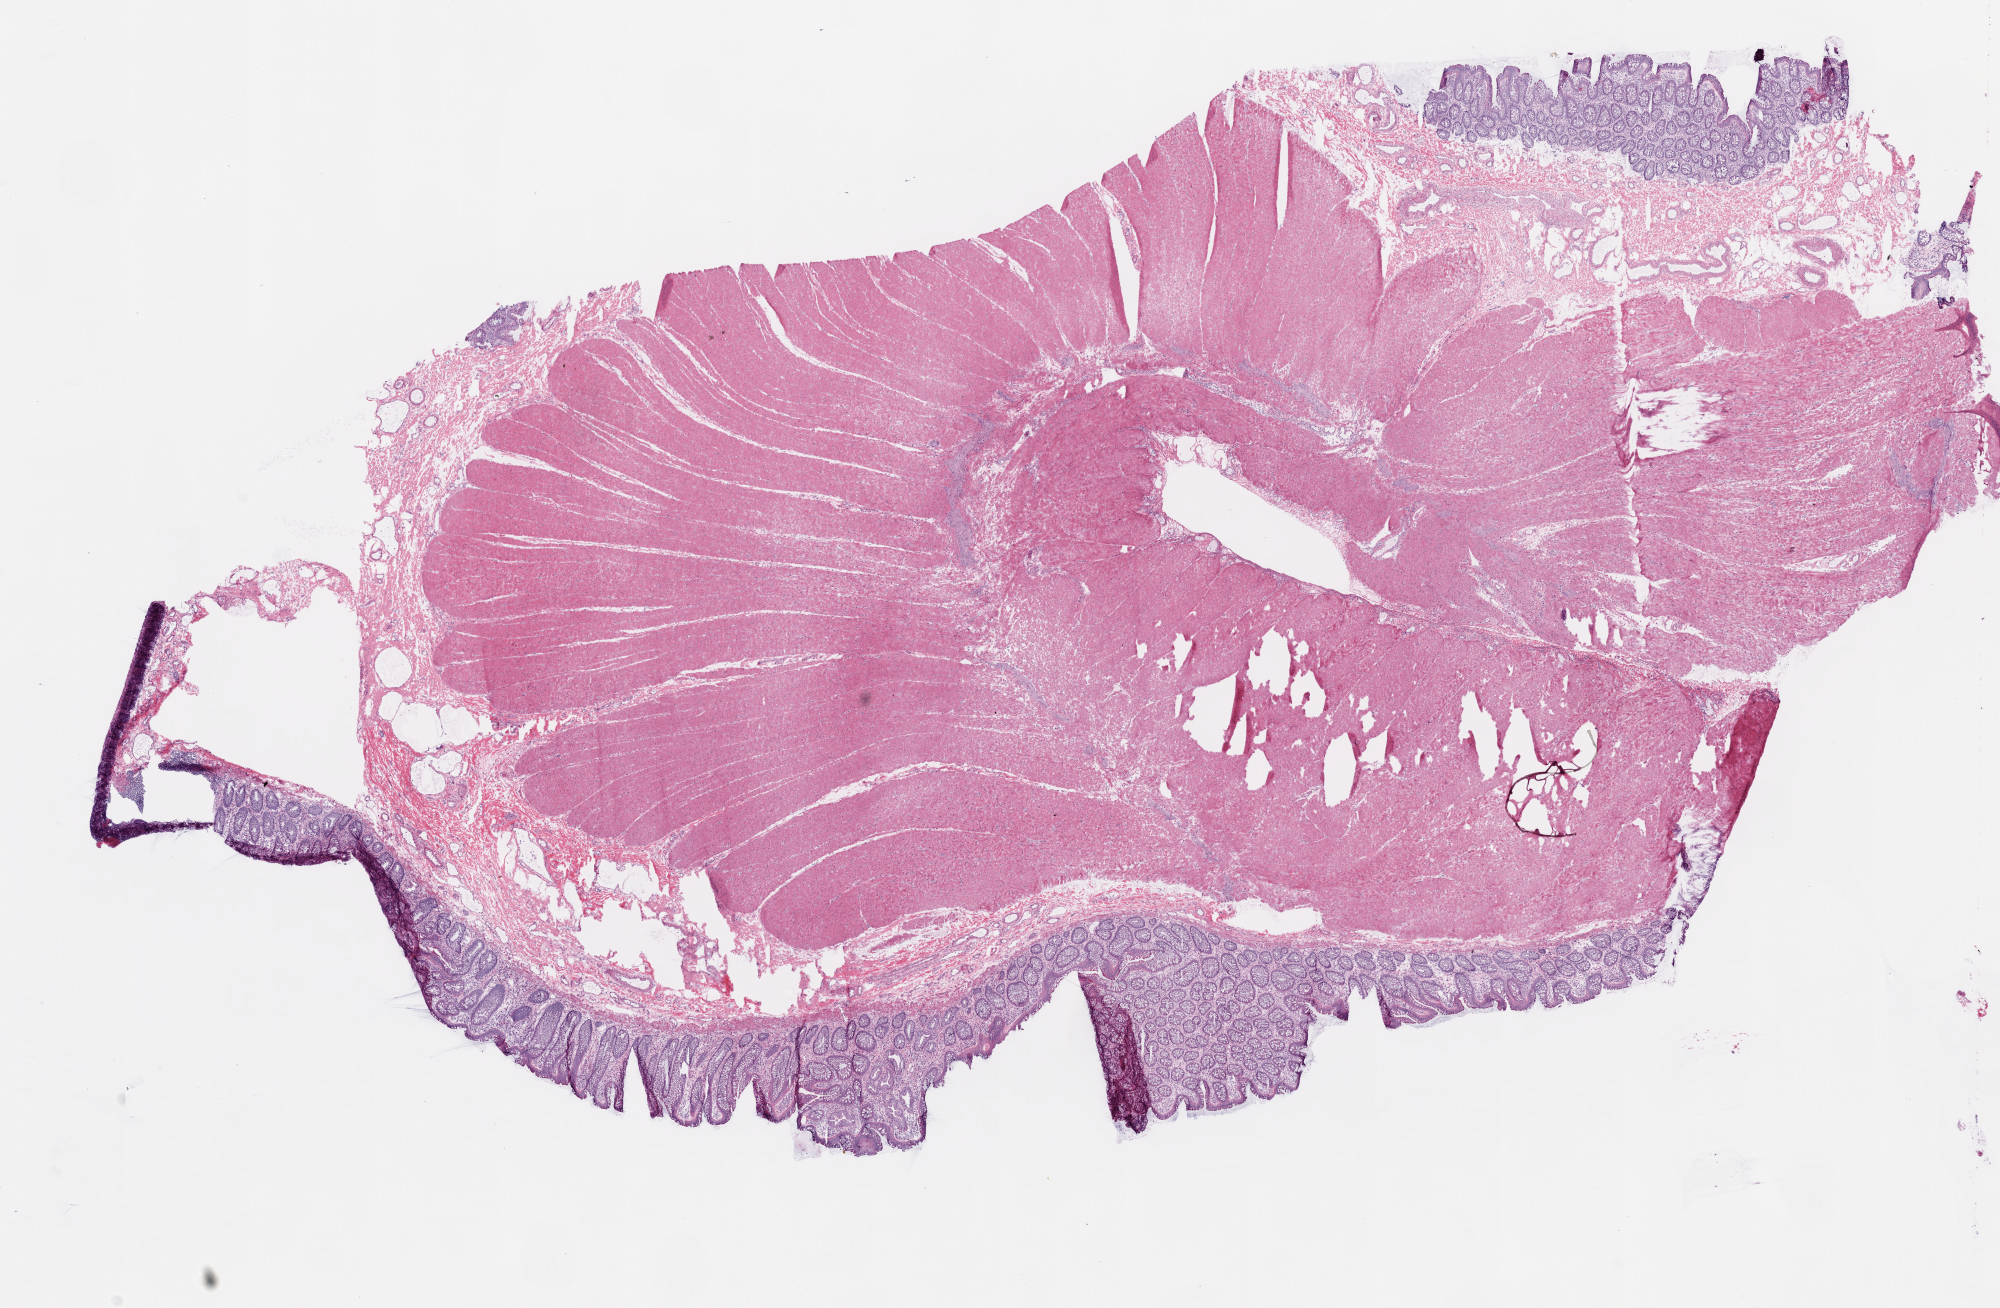
Whole-slide histology image, H&E — low-resolution overview of the scanned area, about 16.0 x 10.5 mm; frozen section from the bottom of the tissue portion; sample: solid tissue normal (non-tumour tissue), colon. Female, age 53 years at initial diagnosis.
This section: solid tissue normal (non-tumour) sample from the same patient. Patient diagnosis: Adenocarcinoma, NOS (sigmoid colon).